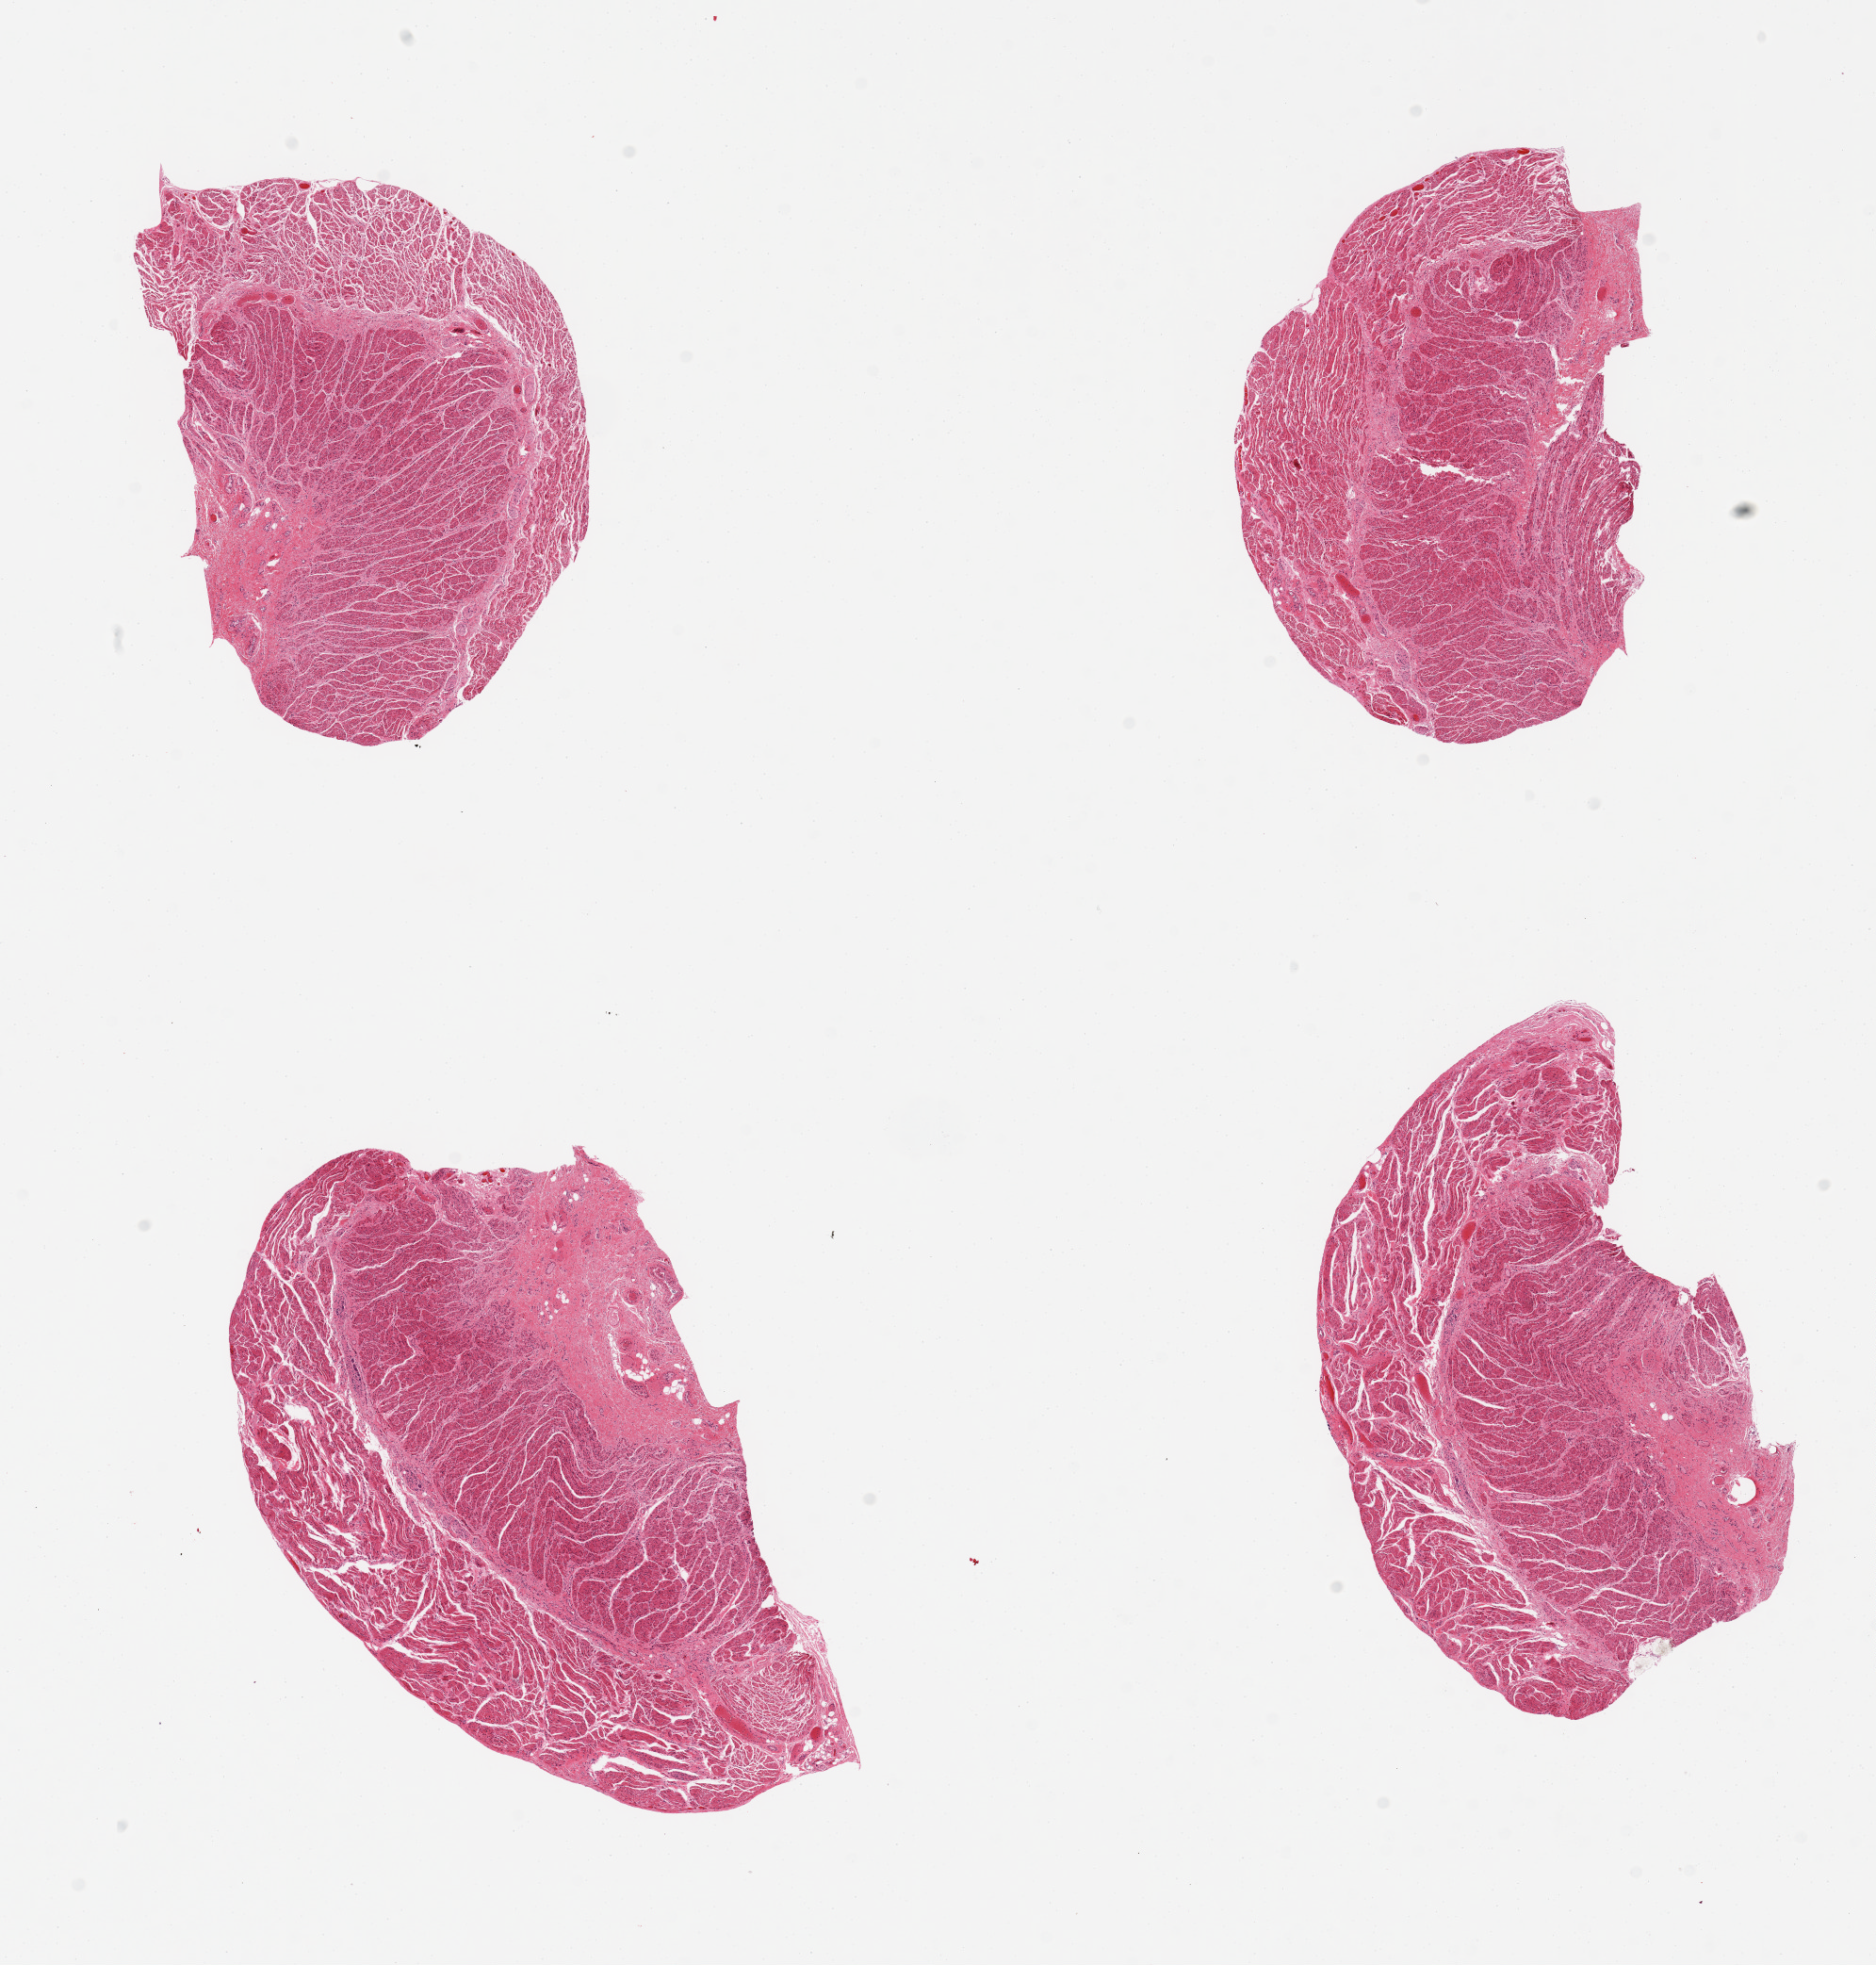
Whole-slide image, haematoxylin and eosin stain — shown as a low-resolution overview of the whole scanned area (about 15.8 x 16.5 mm). PAXgene-fixed, paraffin-embedded tissue. Section of gastroesophageal junction (target tissue). Donor tissue sample. Donor sex: male.
- pathologist's review note for this sample: 4 pieces, well trimmed